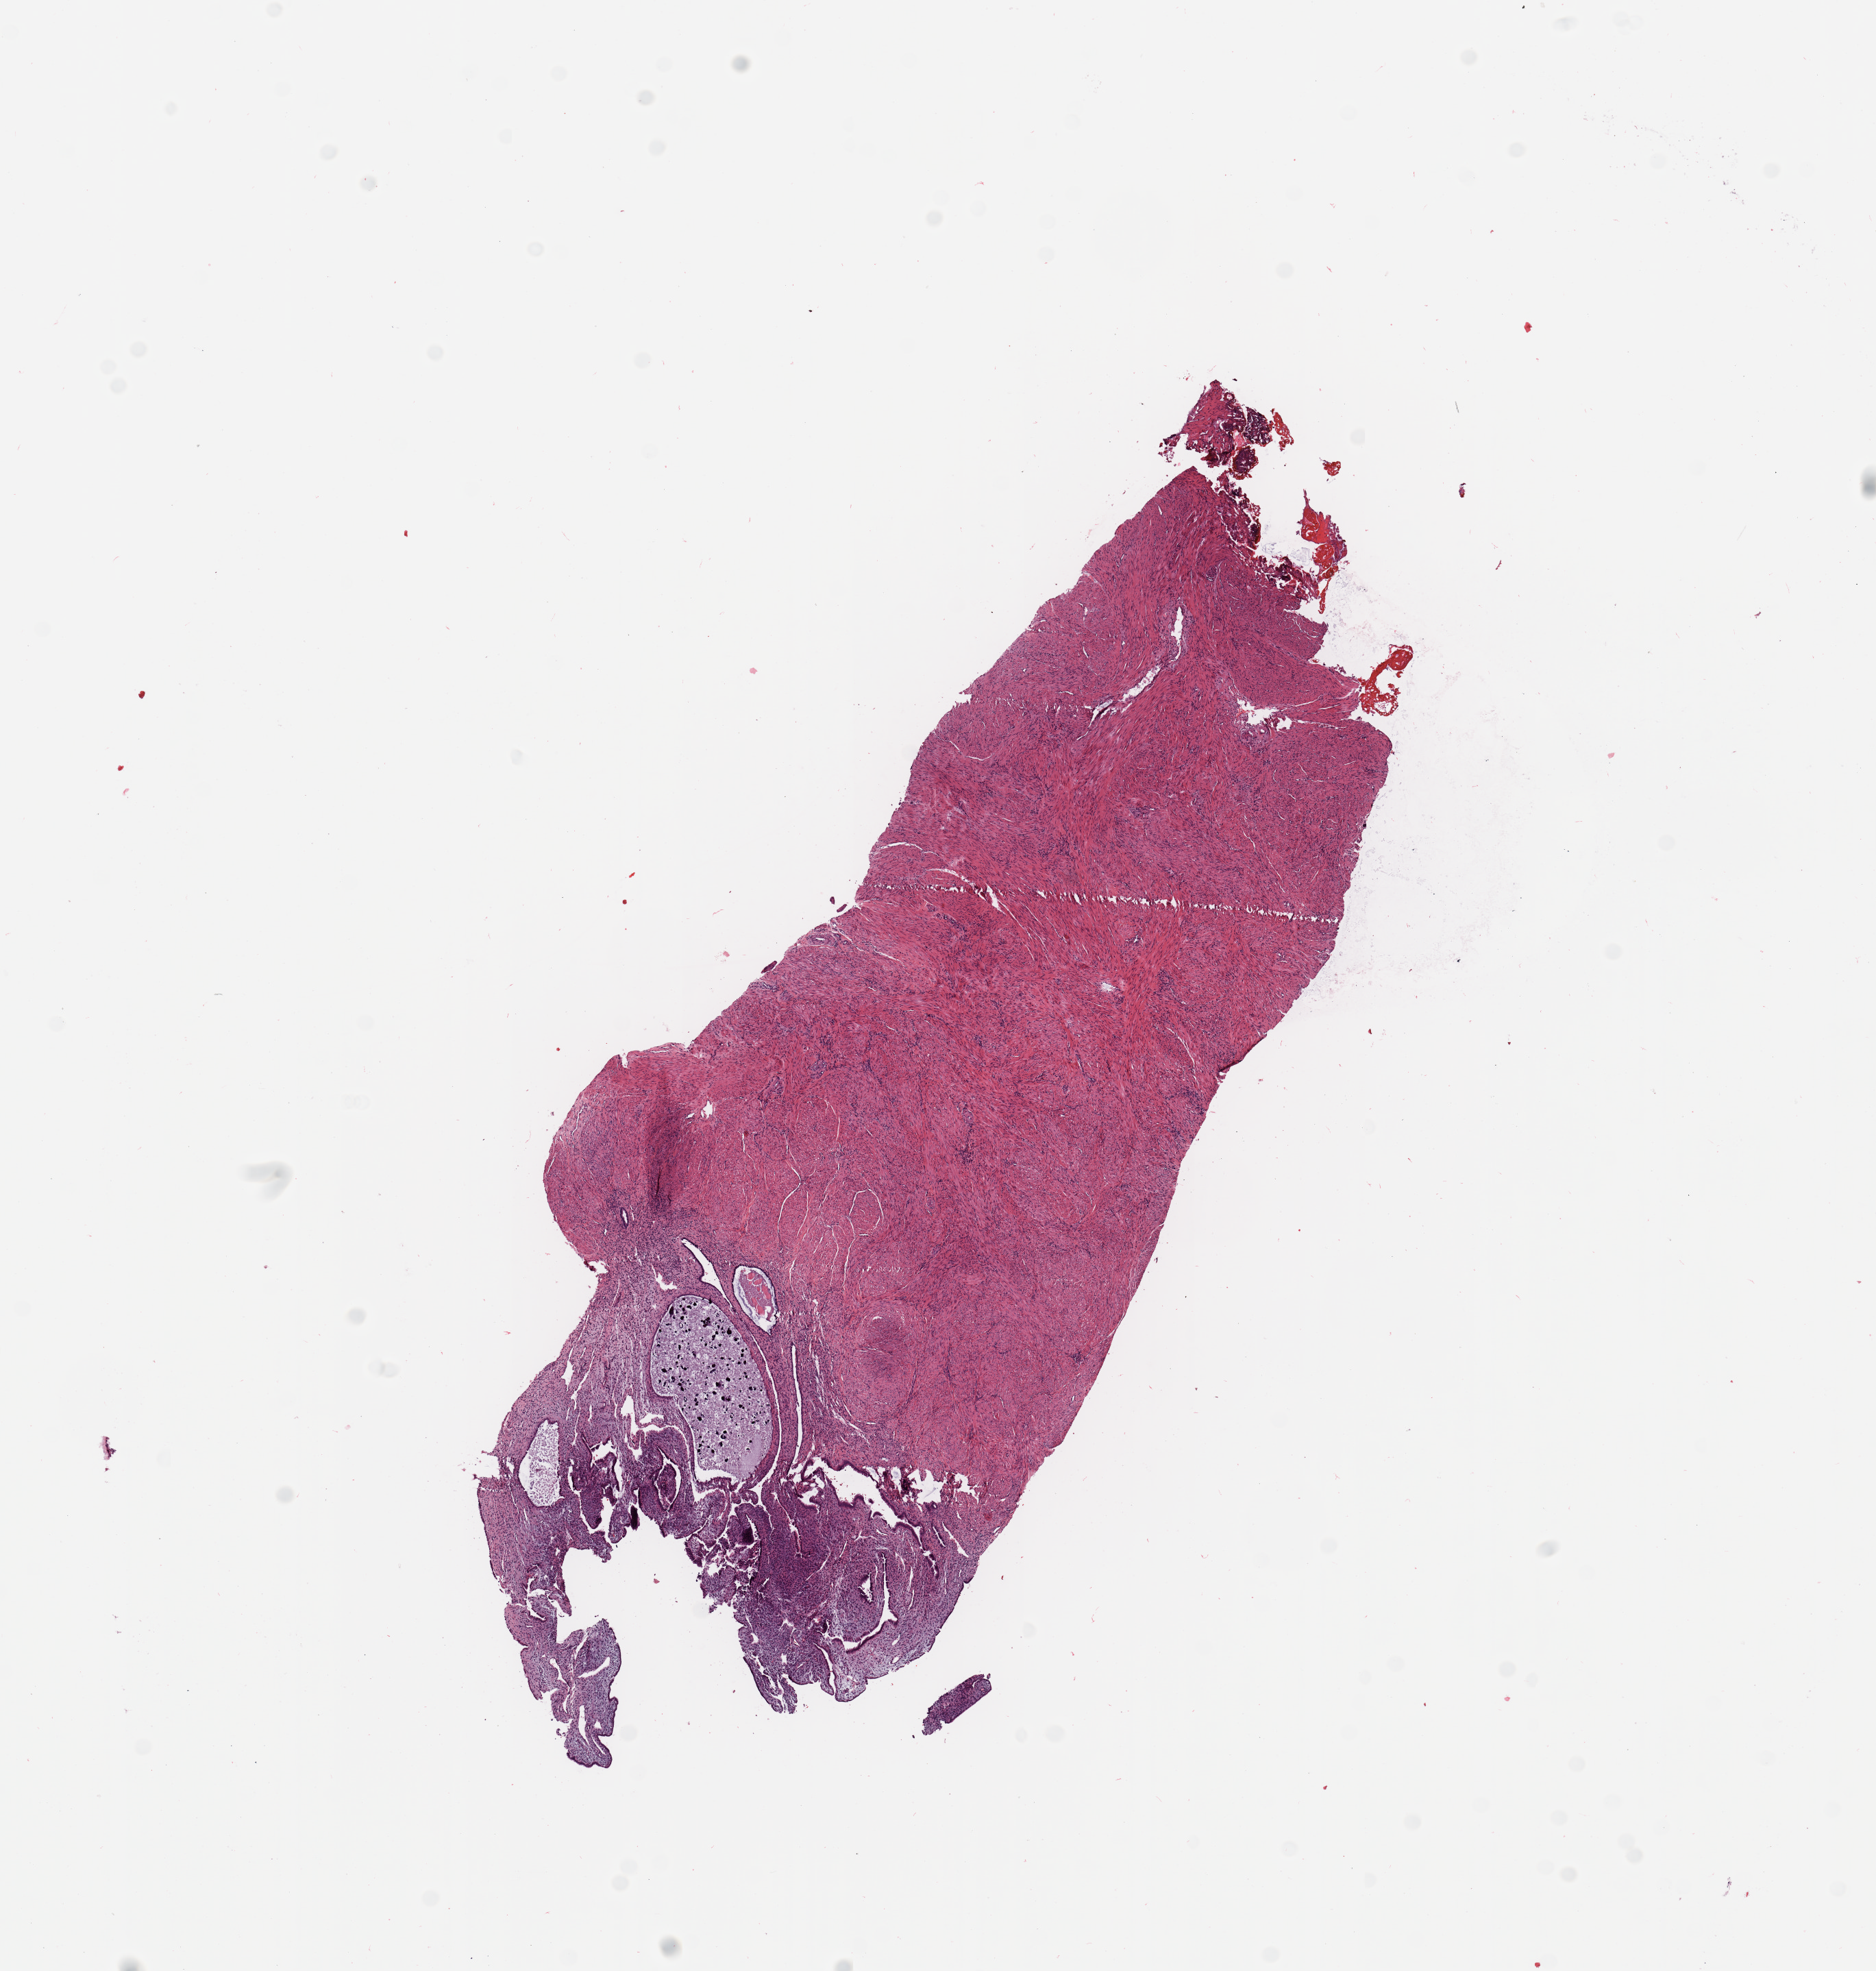
Hematoxylin and eosin (H&E) stained whole-slide image, shown as a low-resolution overview of the whole scanned area (about 10.8 x 11.4 mm, slide scanned at 20x). Normal (non-tumour) tissue sample, sampled site: uterus. Female, 63 y/o.
This section: normal (non-tumour) tissue from the same patient. Patient diagnosis: Endometrioid adenocarcinoma, NOS.